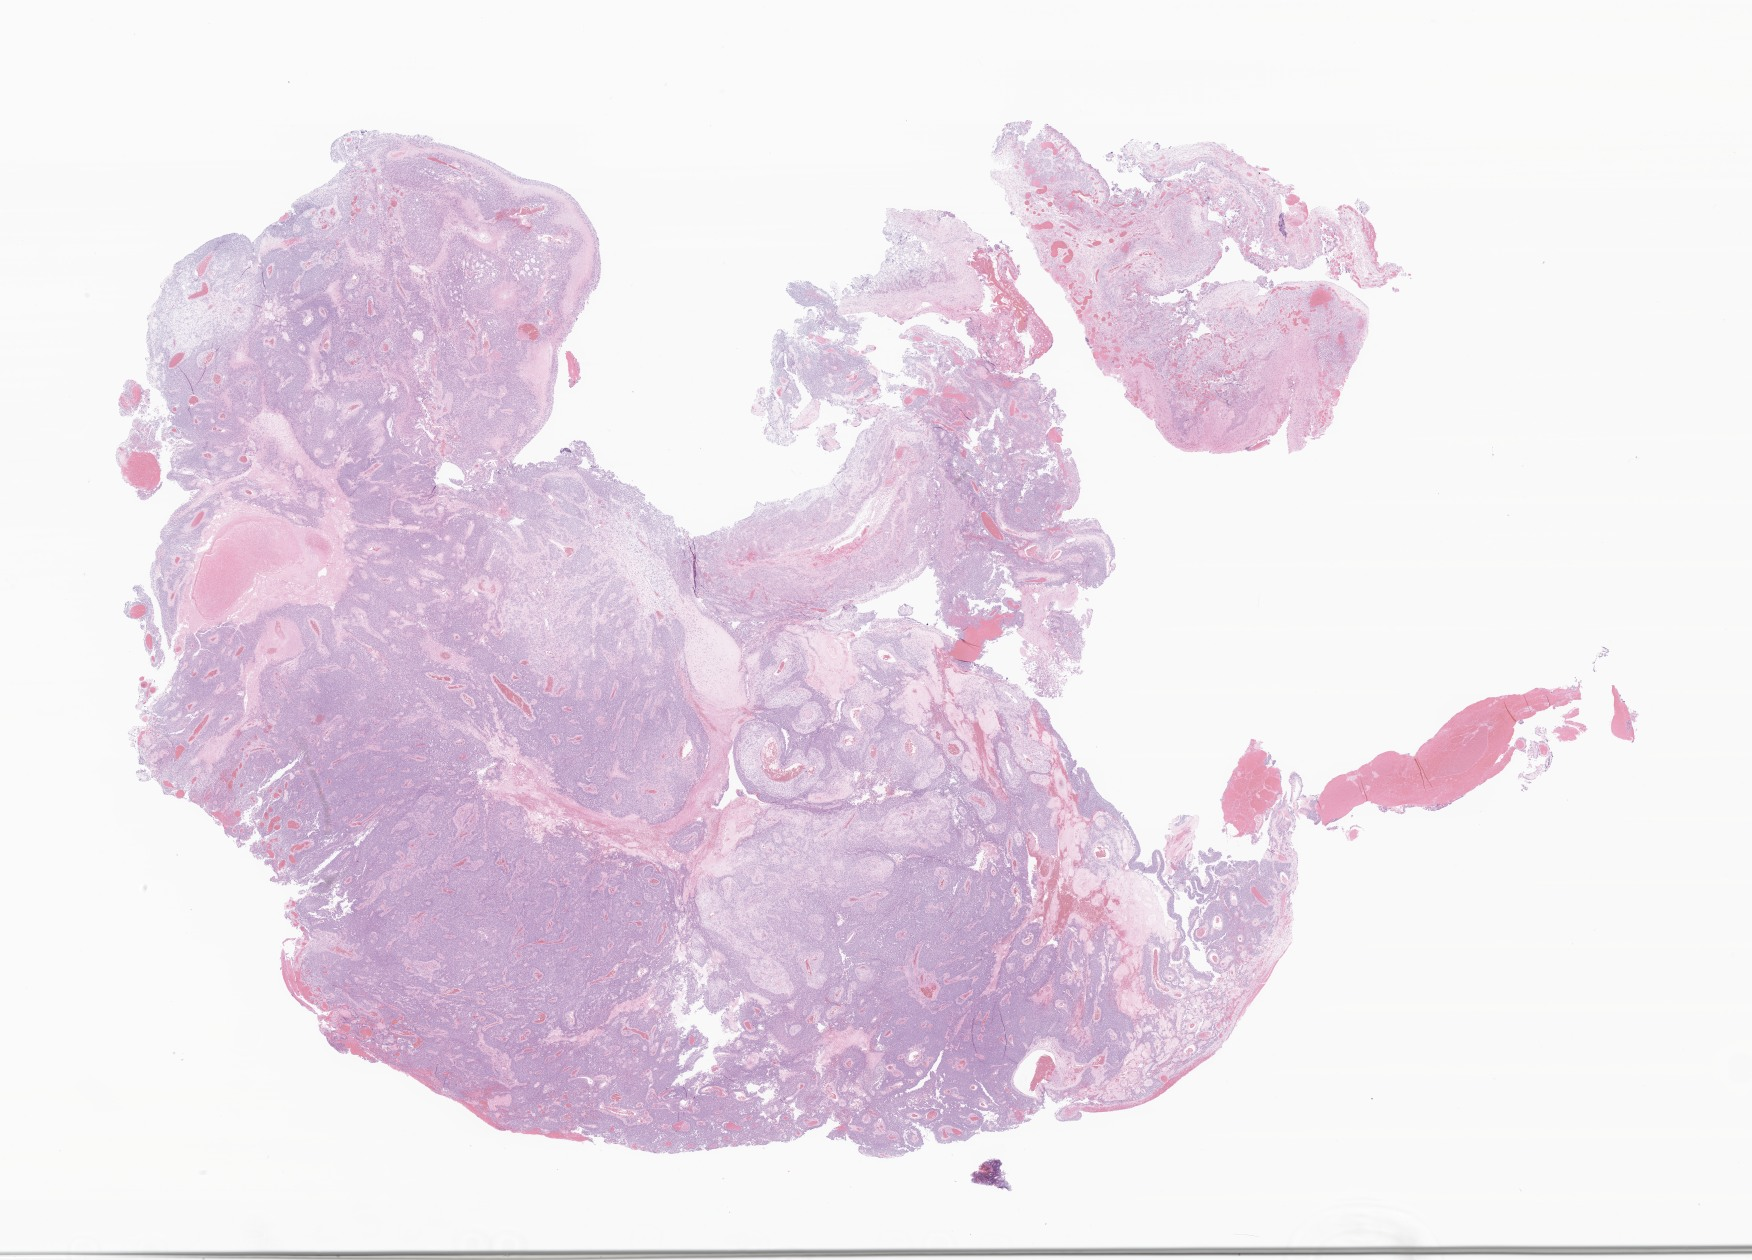
Whole-slide image, H&E stain of tumor tissue from the parietal lobe — low-resolution overview of the scanned area, about 29.6 x 21.3 mm, FFPE section. Patient: female, age 49 months (4 years 1 month).
Recorded diagnosis: Glioma, malignant.